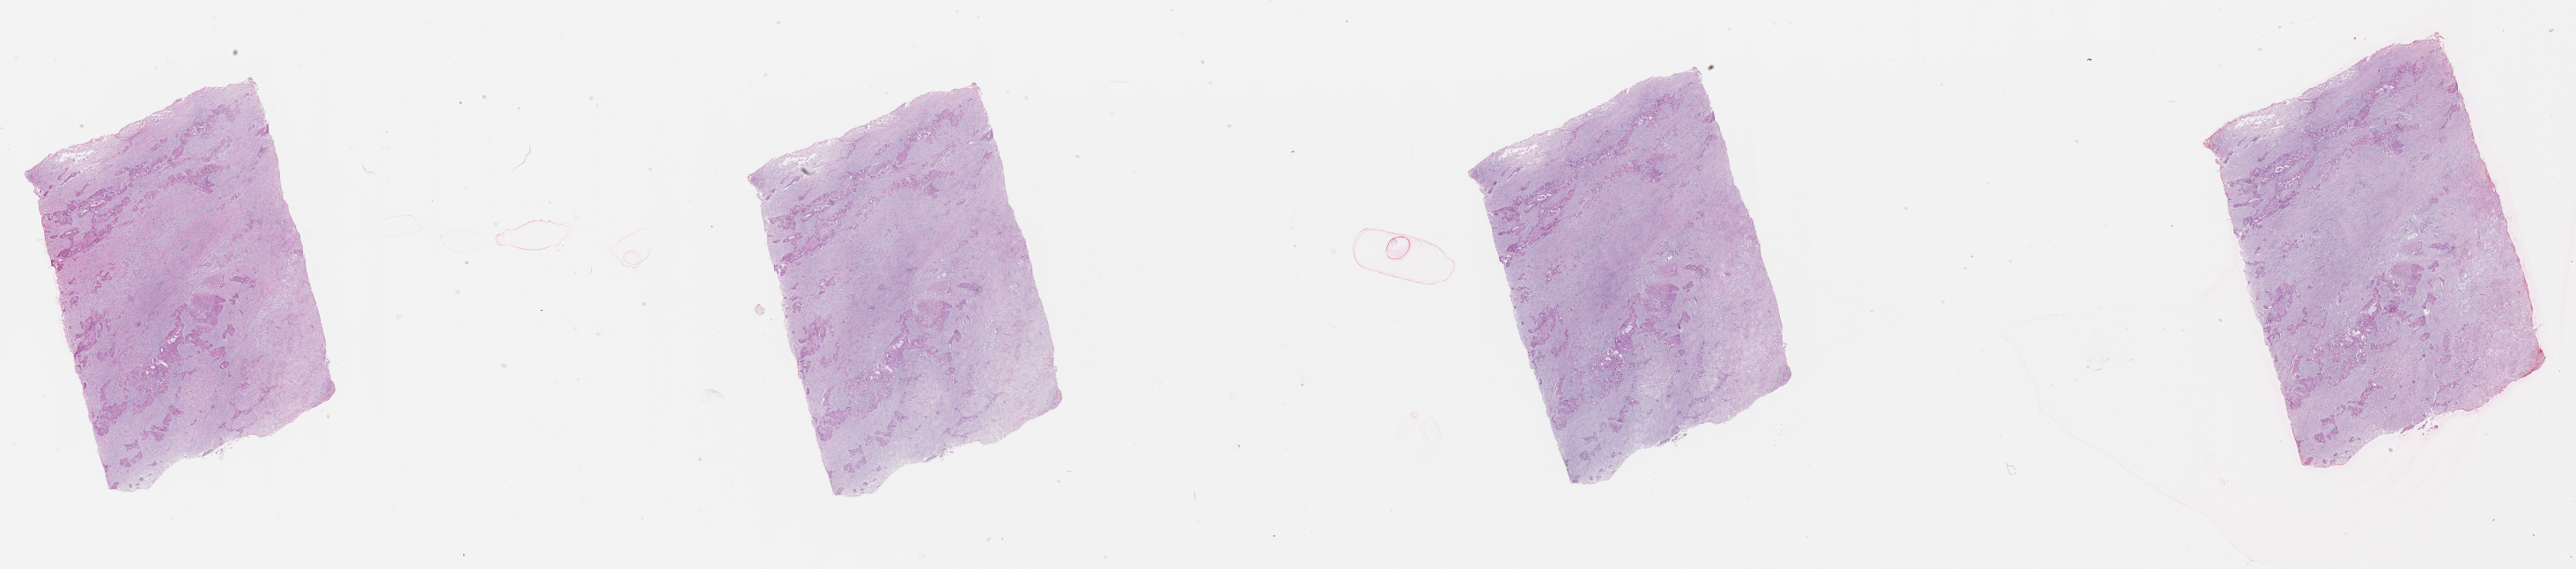
Whole-slide histology image, H&E-stained, shown as a low-resolution overview of the whole scanned area (about 47.1 x 10.4 mm, slide scanned at 20x). Tumour tissue sample, lung. Male, 74 y/o.
* patient diagnosis (cohort enrolment): squamous cell carcinoma (lung)